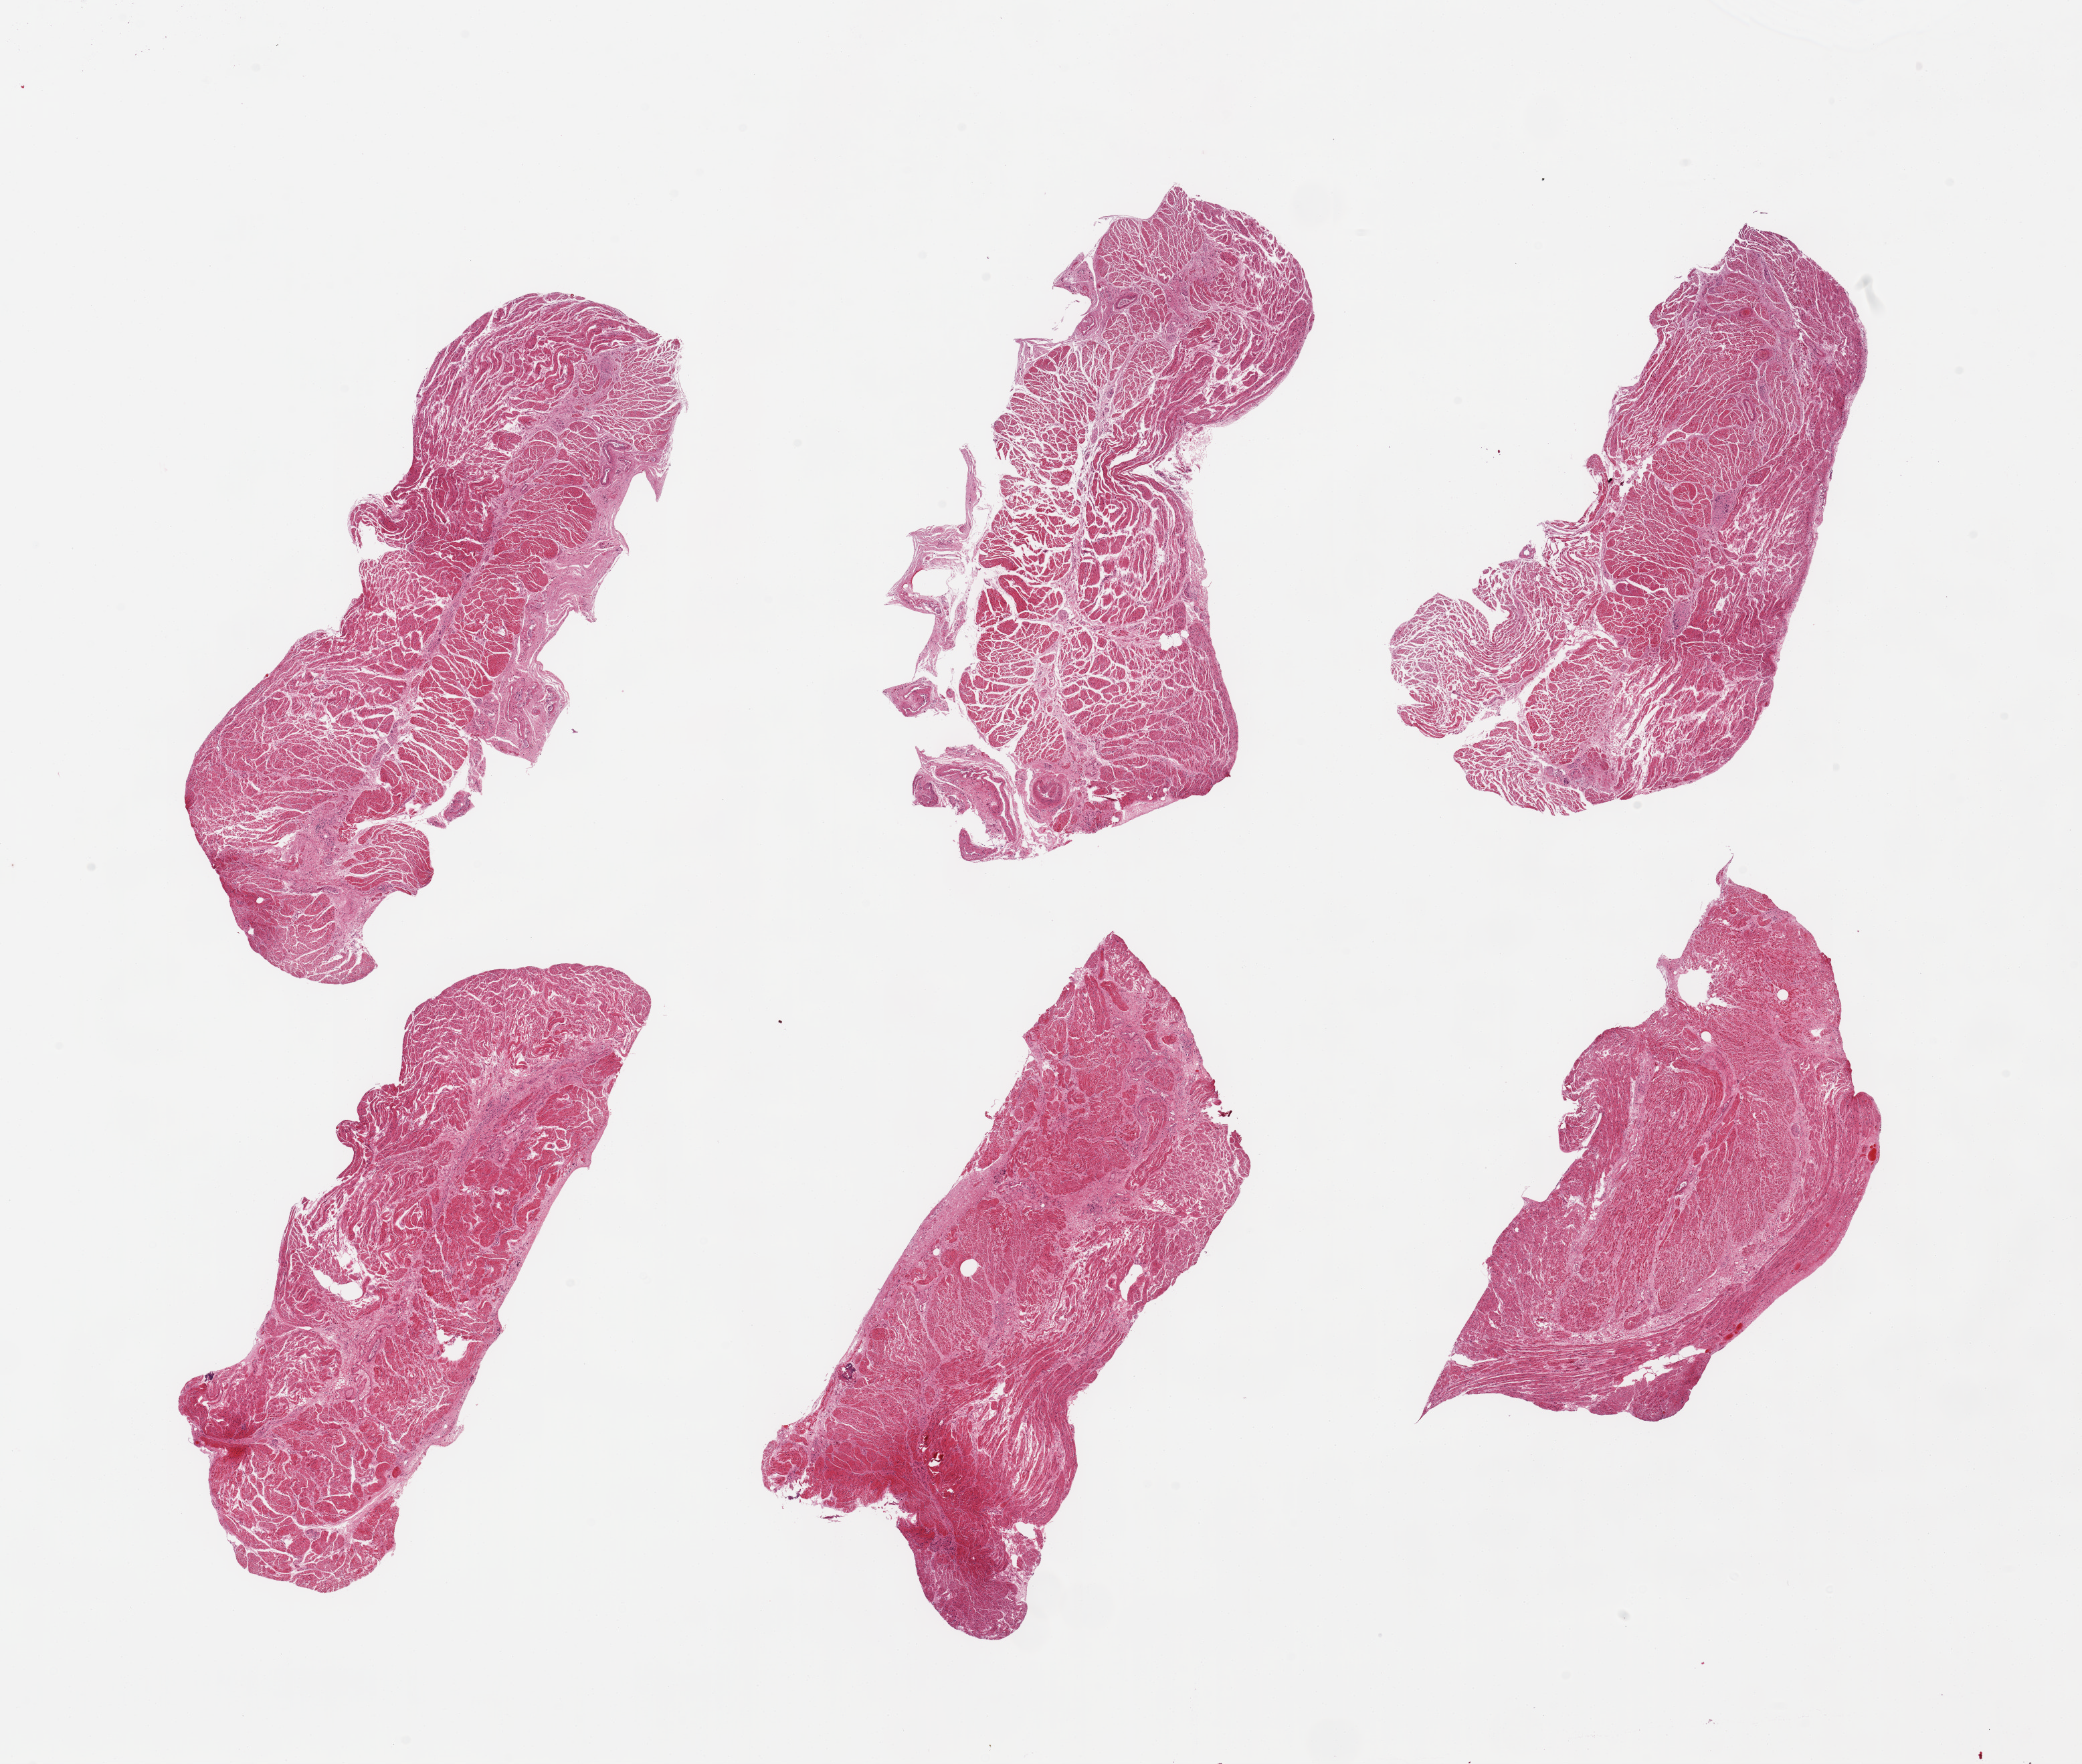
Whole-slide image, H&E stain, brightfield, a low-resolution overview of the entire scanned area, about 24.6 x 20.9 mm (acquisition: 20x scan). PAXgene-fixed paraffin-embedded (PFPE) section. Target tissue: gastroesophageal junction. Donor tissue sample. Donor sex: female.
Reviewer comment on this tissue sample: 6 pieces, confirmed target muscularis.